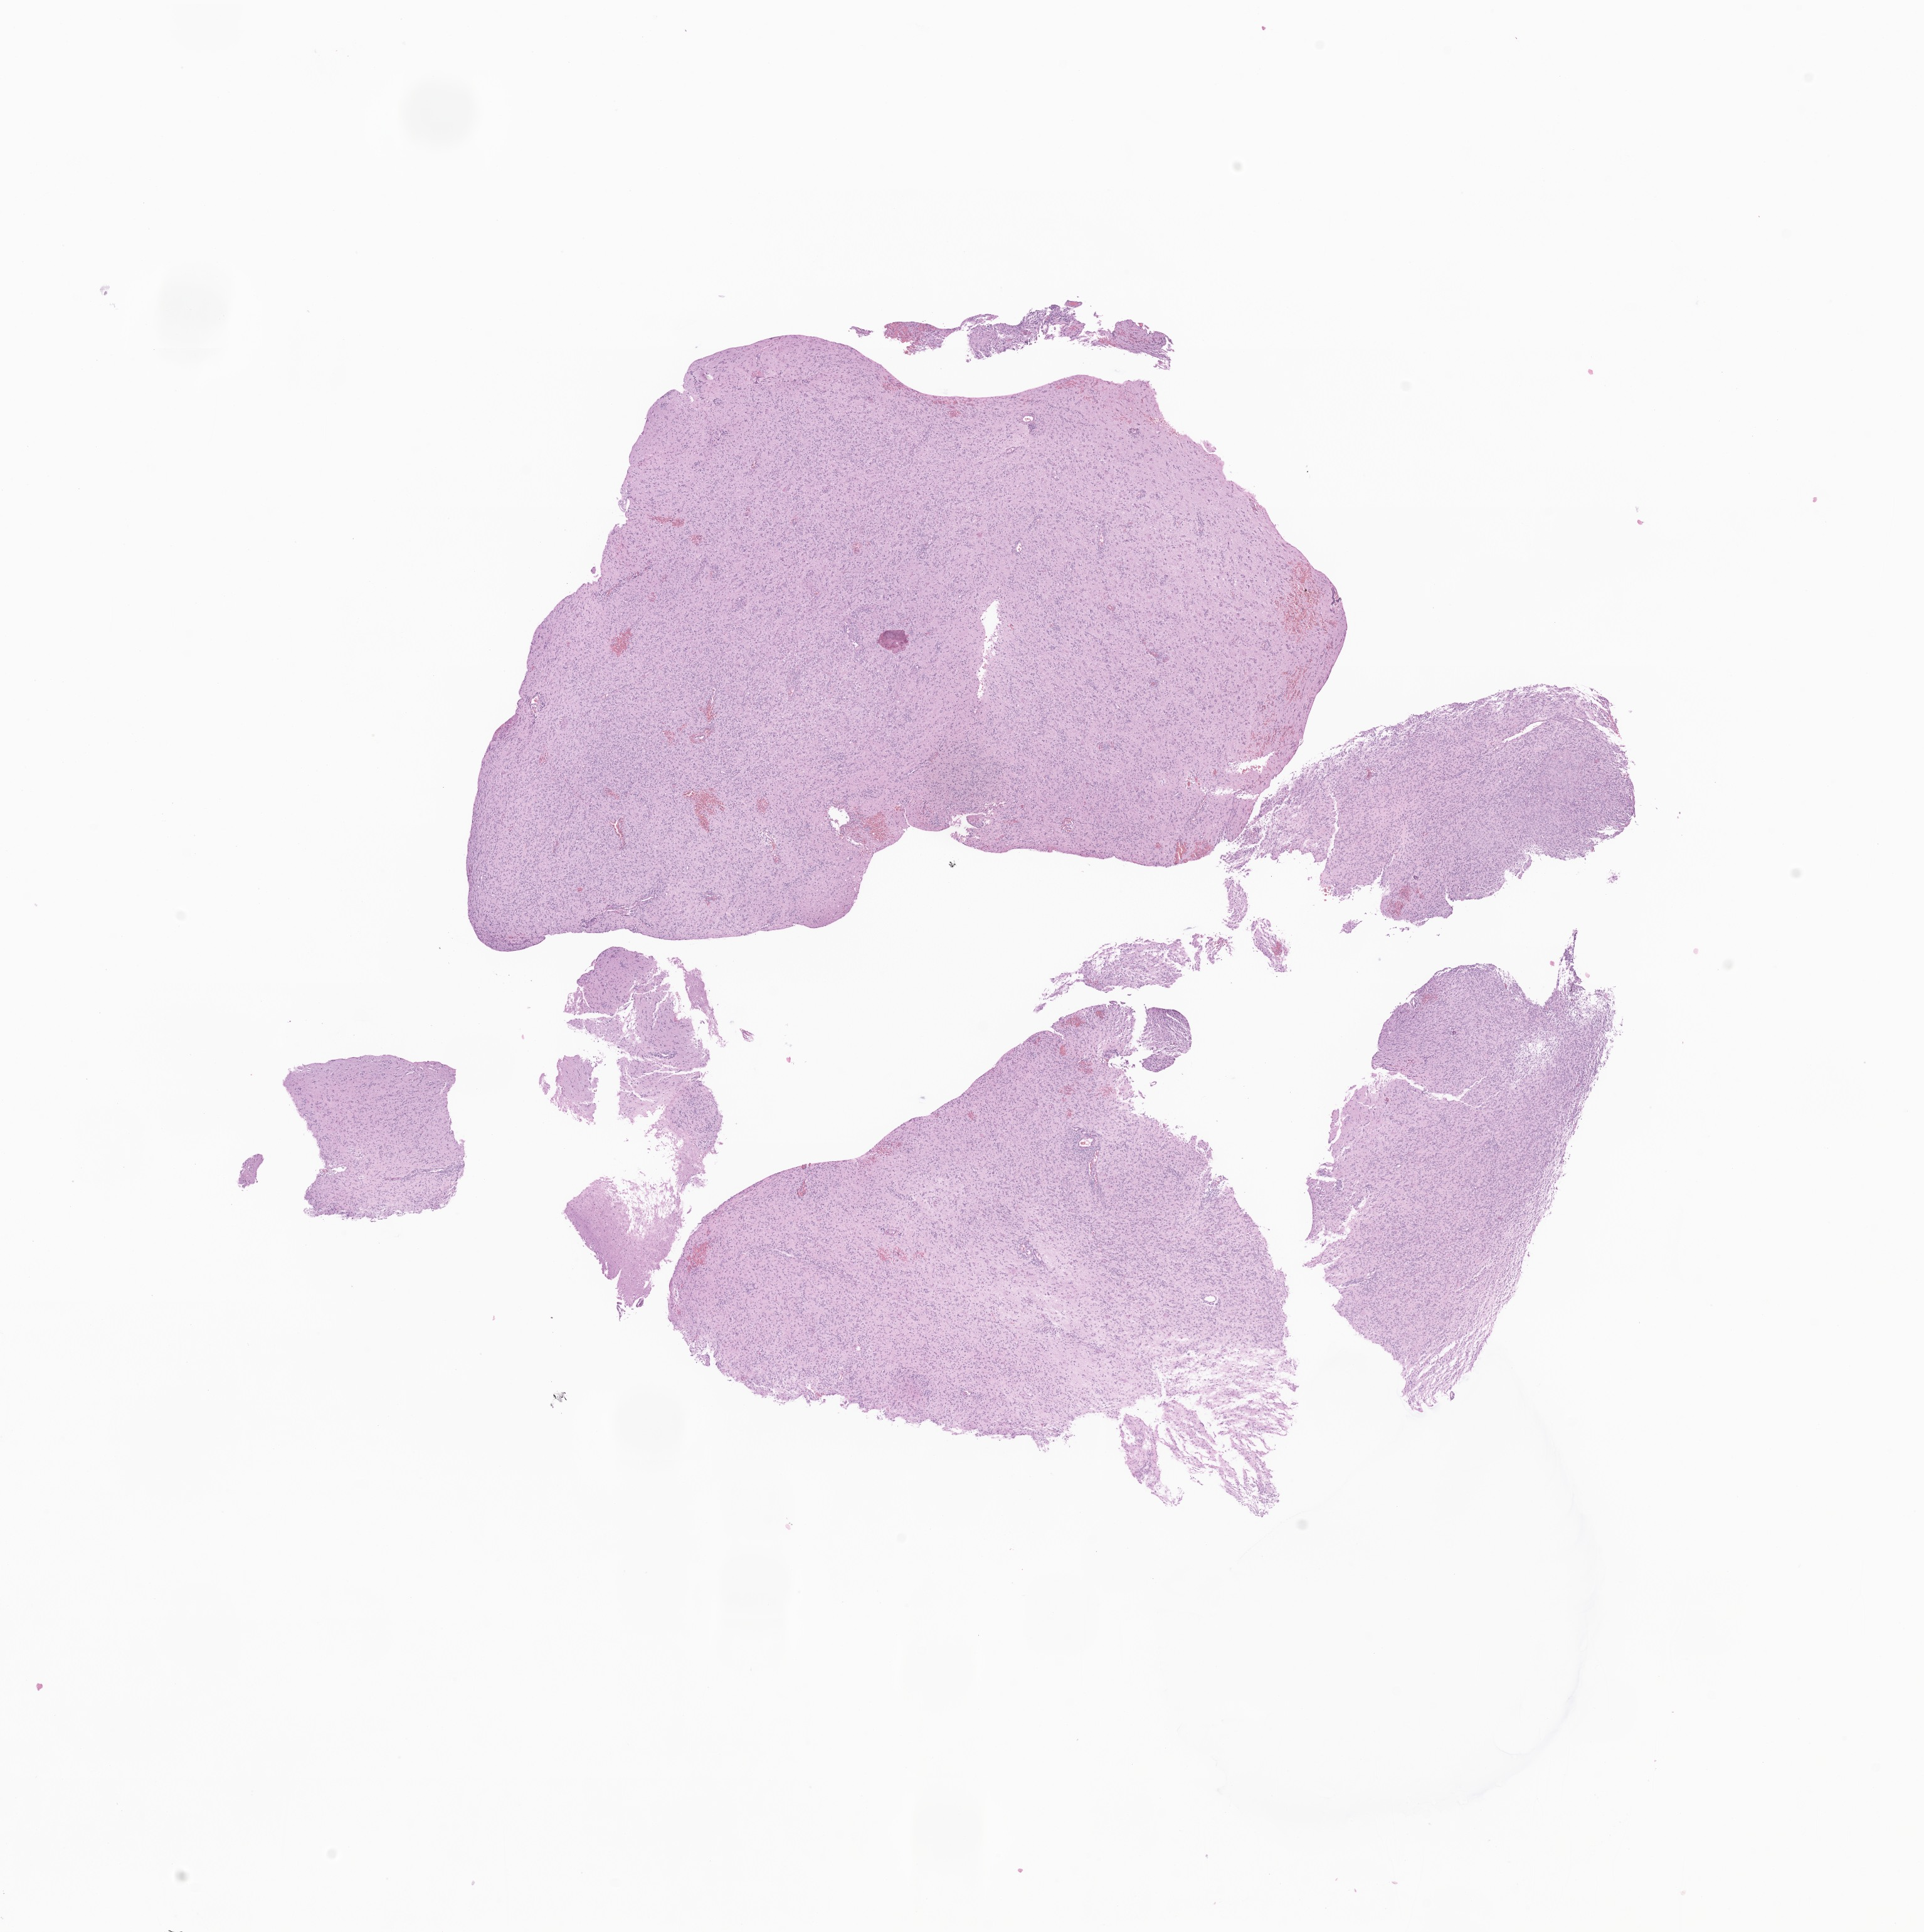
Digitized H&E-stained section of tumor tissue from the frontal lobe — whole scanned area (about 12.9 x 13.0 mm) shown as a low-resolution overview. Formalin-fixed, paraffin-embedded (FFPE) tissue. Female patient, age 126 months (10 years 6 months).
- diagnosis (ICD-O-3 morphology term): Neuroepithelioma, NOS